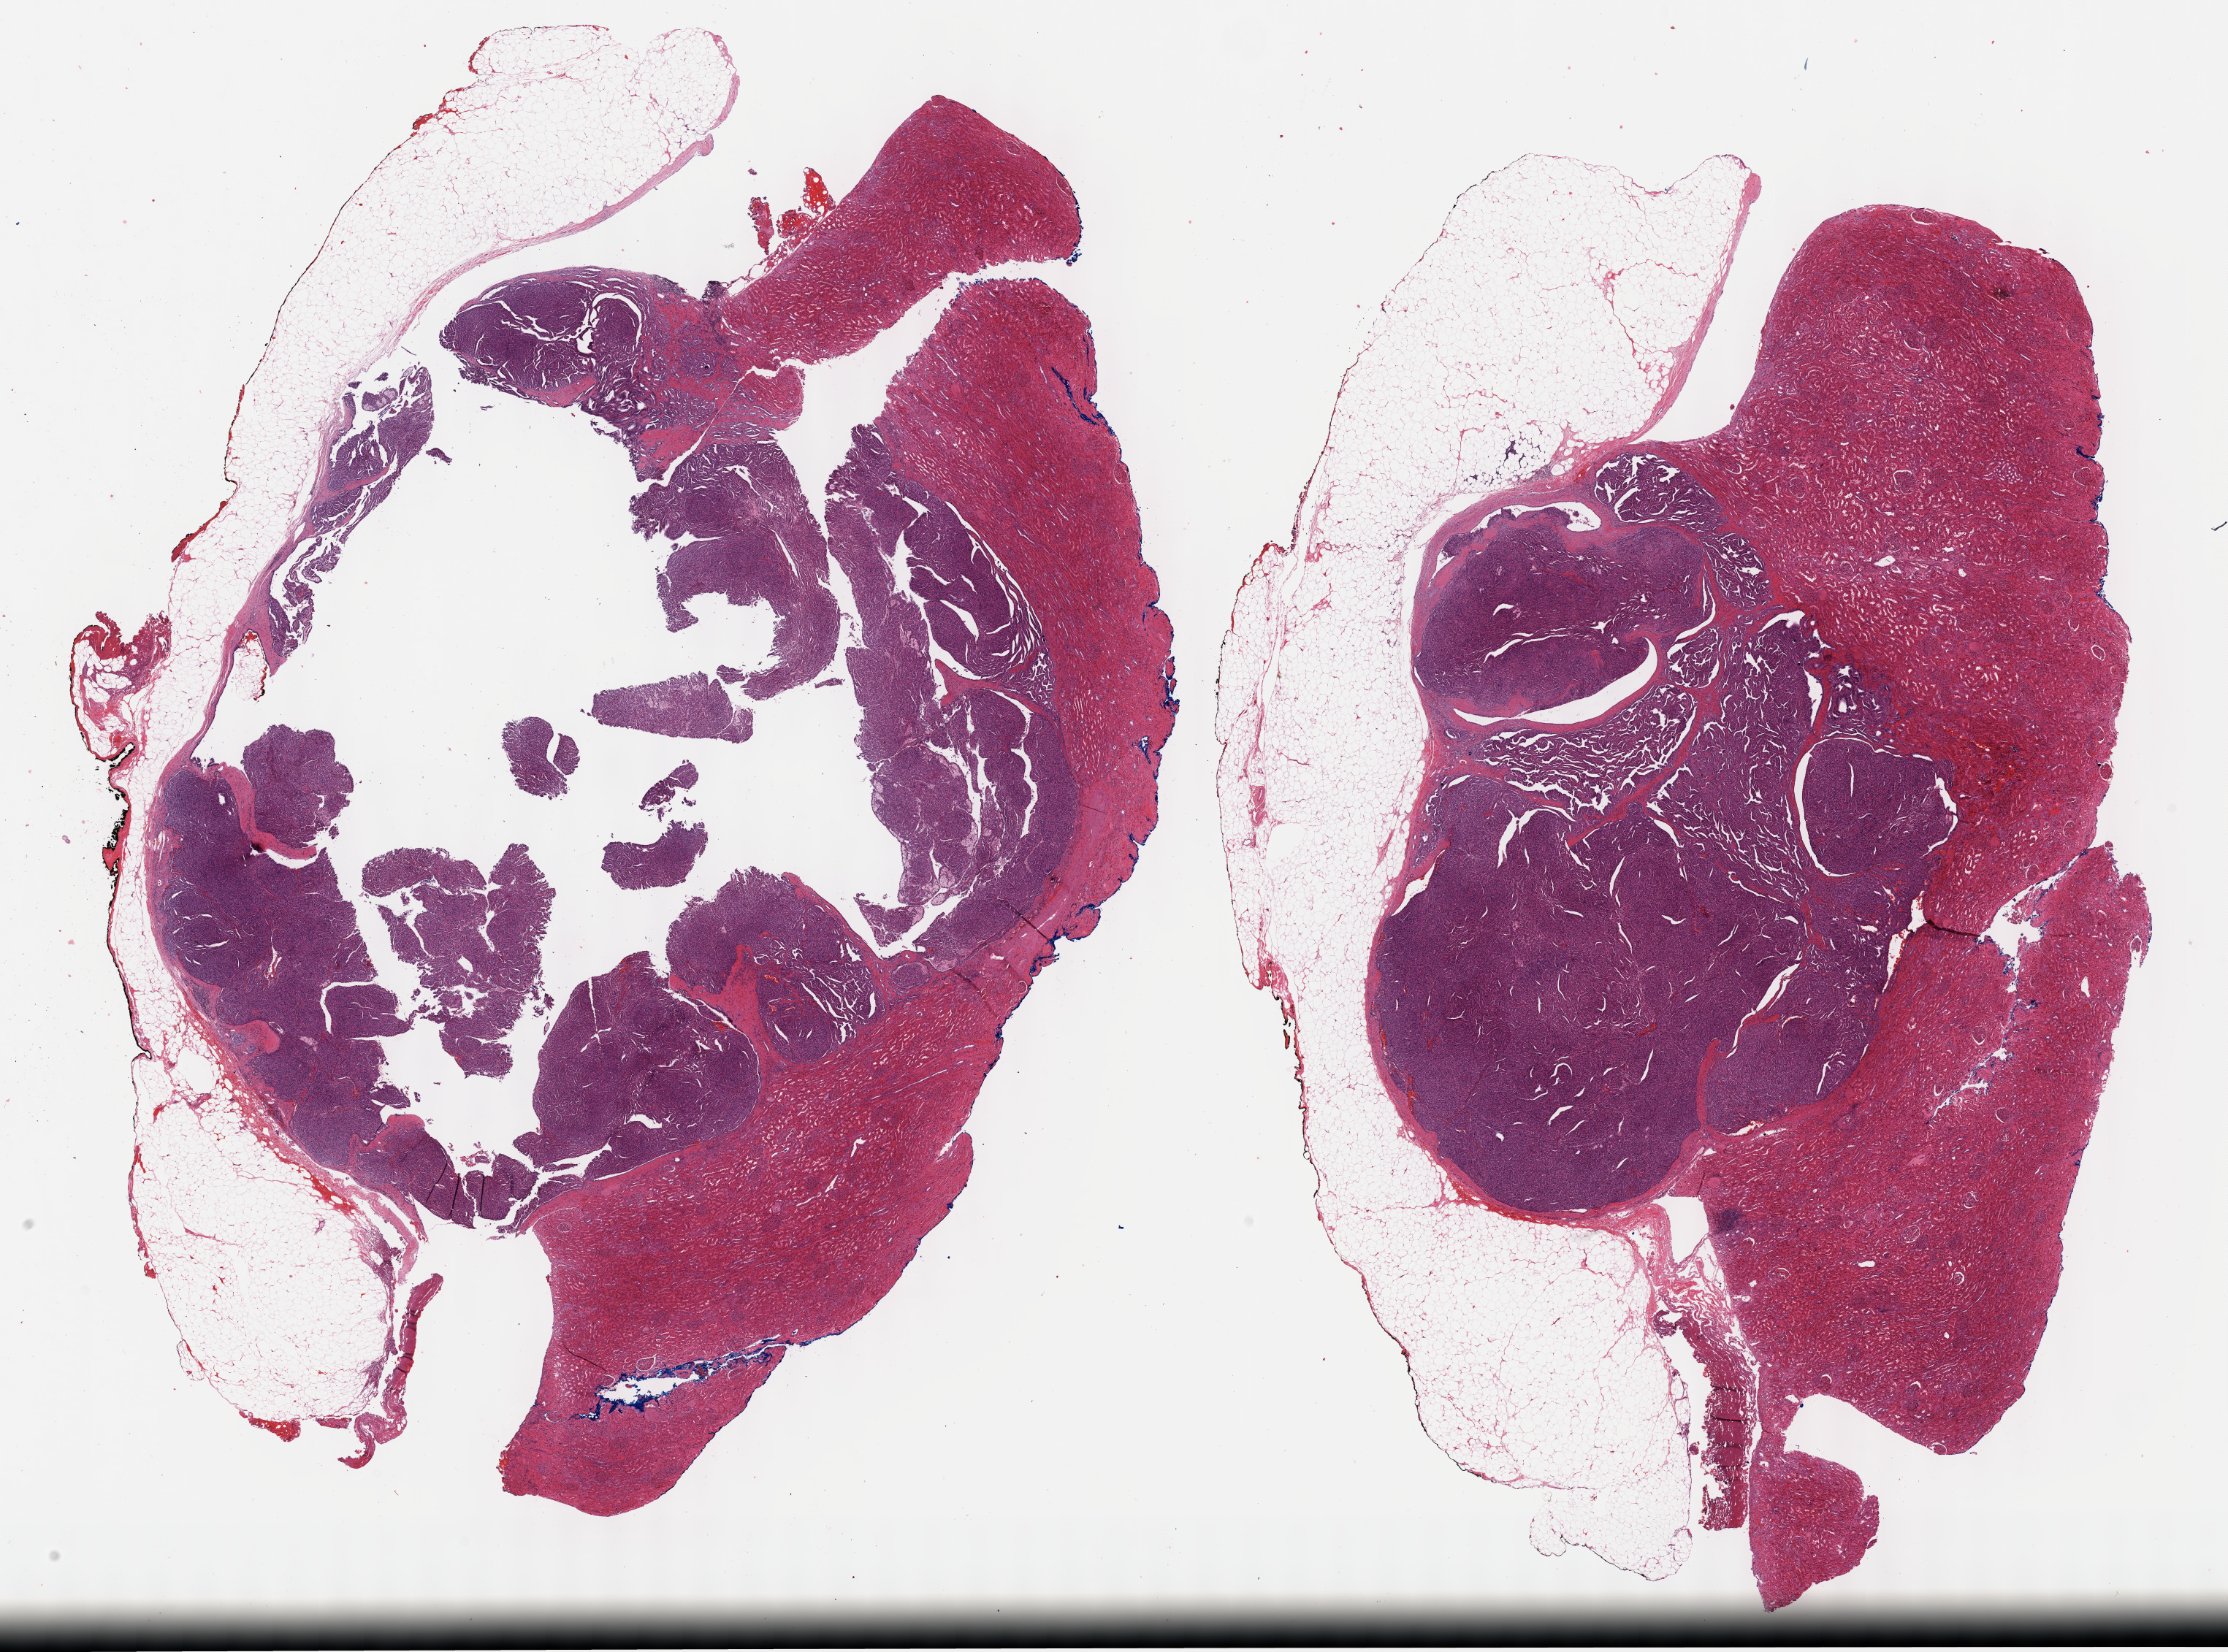
H&E whole-slide image, shown as a low-resolution overview of the whole scanned area (about 24.7 x 18.3 mm, from a 40x scan). Formalin-fixed paraffin-embedded (FFPE) diagnostic section. Sample: primary tumour, kidney. Male patient; age at initial diagnosis 58 years.
• AJCC pathologic stage: I (7th edition)
• laterality: left
• pathologic diagnosis: Papillary adenocarcinoma, NOS